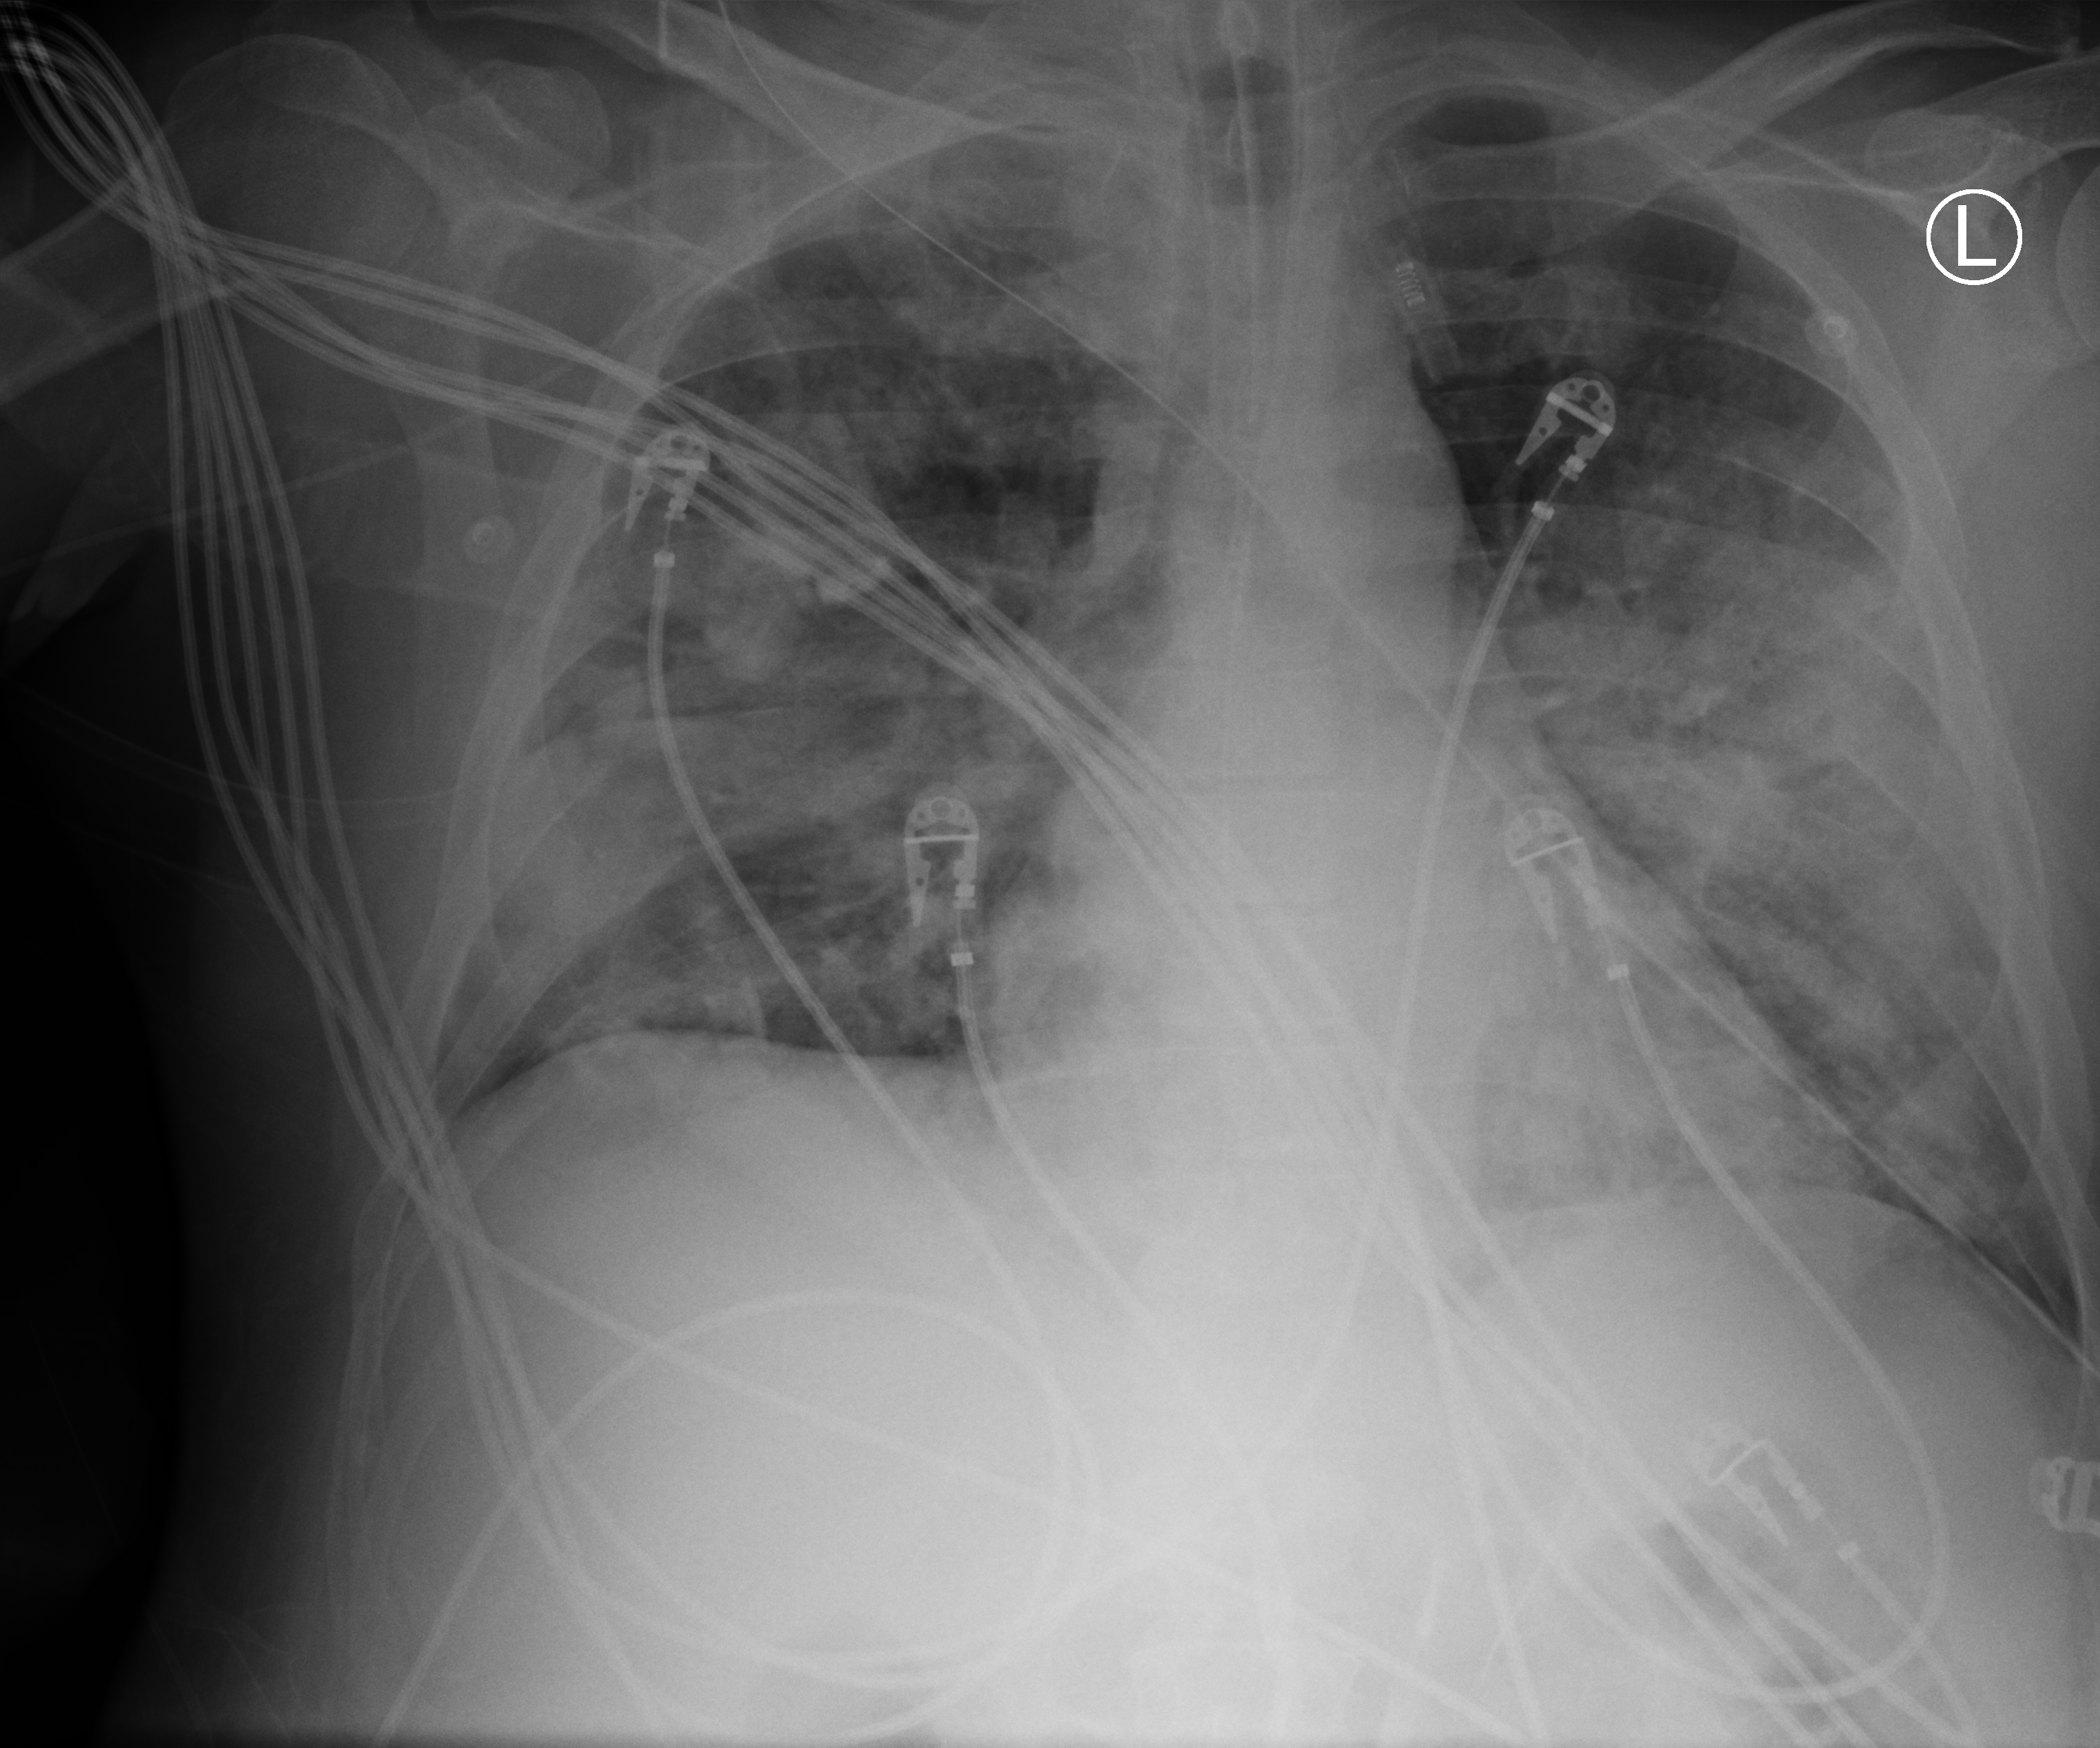
Chest X-ray (portable), anteroposterior (AP) projection. Patient hospitalised with COVID-19; male, aged 18–59 years.
Admission-level facts for this patient (not findings on this image; timing relative to this image not recorded):
- mechanically ventilated during this hospital stay: yes